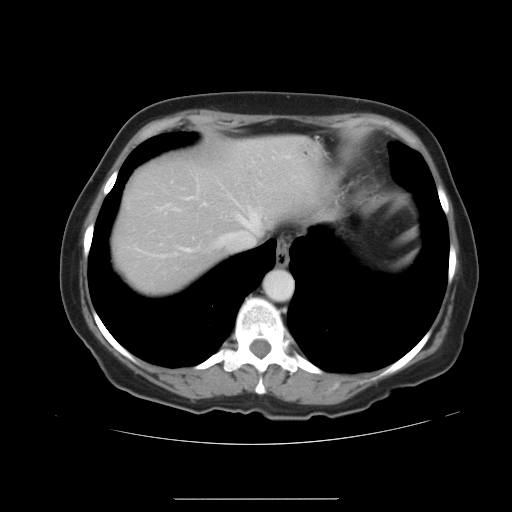
Contrast-enhanced abdominal CT, one axial slice. Position 33 of 41 along the scan axis. Intravenous contrast given. Soft-tissue window (W 400 / L 40 HU). 512 × 512 image matrix, field of view 381 × 381 mm. Female patient, age 63 years. From the clinical record (not read from this slice): diagnosis: colorectal cancer liver metastases, imaged before liver resection; multiple liver metastases: yes; largest metastasis: 1.5 cm; disease in both lobes: yes.
Annotated regions visible in this slice (outlined manually by an expert reader):
- hepatic veins: bounding box <183,157,274,250> (left, top, right, bottom; pixels)
- liver: <112,137,313,297>
- planned liver remnant (the part of the liver to remain after resection): <112,137,313,297>
- liver metastasis: <244,180,249,184>